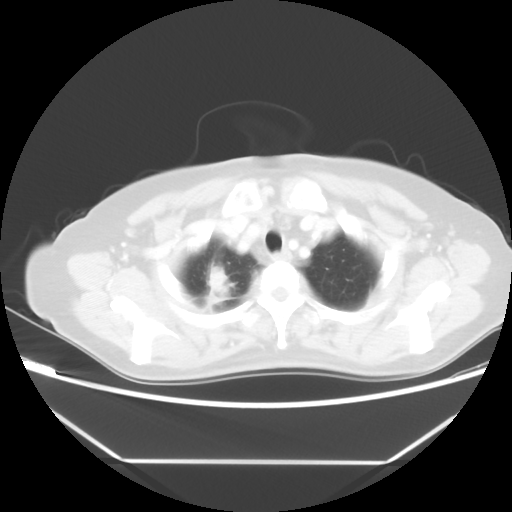
Chest CT, one axial slice. Slice 44 of 48 in the series (ordered by position). Lung window (W 1500 / L -600 HU). 5 mm slice thickness. 512 × 512 image matrix, field of view 360 × 360 mm. Patient: female, 65 years. Case-level facts recorded for this patient, not image findings: clinical TNM (as recorded): T1c N1 M1.
Outlined on this slice (bounding box drawn by a radiologist):
- lung tumour (recorded histology: adenocarcinoma): bounding box [x1, y1, x2, y2] px = [198, 266, 229, 312]